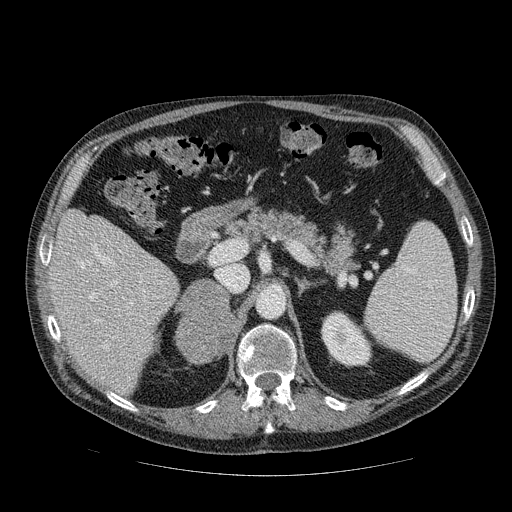
Contrast-enhanced abdominal CT, one axial slice. Position 55 of 111 along the scan axis. Reconstruction kernel STANDARD. Intravenous contrast given. Soft-tissue window (W 400 / L 40 HU). 512 × 512 image matrix, field of view 420 × 420 mm. Patient: male, 56 years. From the clinical record (not read from this slice): diagnosis: adrenocortical carcinoma; tumour side: right adrenal.
Structures marked on this image (semi-automatically segmented with operator editing):
- mass: bounding box [x1, y1, x2, y2] px = [177, 280, 236, 363]